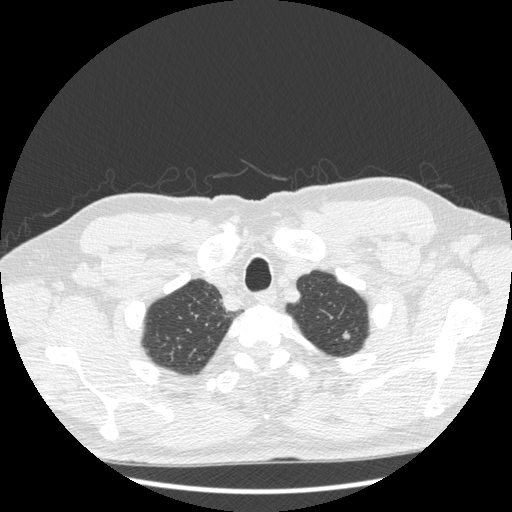
Low-dose screening chest CT, axial slice, third screening round (two years after baseline), lung window (W 1500 / L -600 HU), 1.25 mm slice thickness, slice 28 of 223 in the series. Male, age 69 years at enrolment.
Lesion marked by an expert reader, bounding box <331,323,357,347> (left, top, right, bottom; pixels). Reader record for this screening exam (exam-level; its link to the box is not recorded): non-calcified nodule or mass ≥4 mm, left upper lobe, 7 × 6 mm, smooth margins, soft tissue attenuation, pre-existing on the prior screen: yes; interval growth: yes. Later outcome: lung cancer diagnosed 112 days after this screen — adenocarcinoma, NOS, left upper lobe, moderately differentiated (G2), stage IA (AJCC 6th edition), 10 mm at pathology.